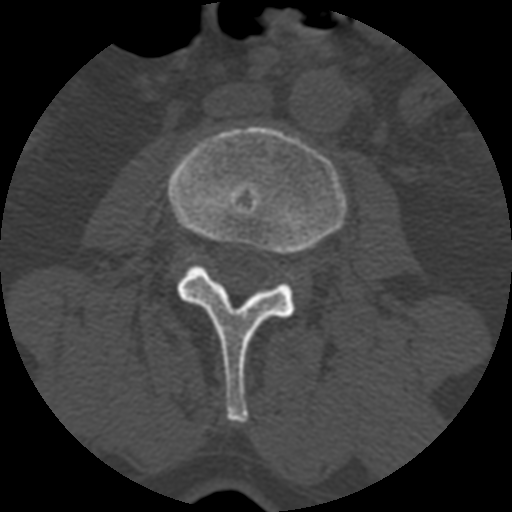
CT including the spine, one axial slice; position 301 of 399 along the scan axis; reconstruction kernel STANDARD; 120 kVp; bone window (W 1800 / L 400 HU); 1.25 mm slice thickness; 512 × 512 image matrix, field of view 160 × 160 mm. Patient age 71 years. Case-level facts recorded for this patient, not image findings: primary cancer: prostate.
Structures marked on this image (semi-automatic segmentation, software-assisted and operator-edited):
- L3 vertebra: bounding box (x1, y1, x2, y2) in pixels: (168, 127, 346, 422)